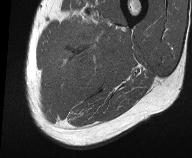
MRI of an extremity soft-tissue mass, one axial slice; position 13 of 61 along the scan axis; MR volume resampled by the dataset authors to the PET/CT grid (not the native acquisition matrix); 3.27 mm slice thickness; 192 × 158 image matrix, field of view 187 × 154 mm. Male patient. From the clinical record (not read from this slice): histological type: pleiomorphic liposarcoma; grade: high; site of the primary tumour: left thigh.
Structures marked on this image (expert contour drawn on MRI and transferred to this co-registered scan by the dataset authors):
- gross tumour volume including surrounding oedema: bounding box [x1, y1, x2, y2] px = [57, 16, 119, 86]
- gross tumour volume (mass): [79, 66, 83, 68]